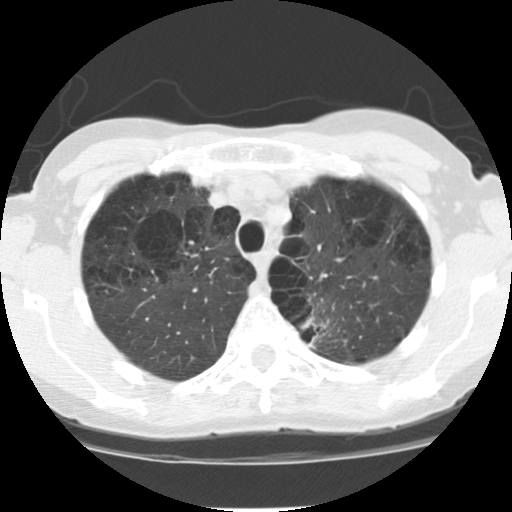
Low-dose screening chest CT, one axial slice. Position 92 of 116 along the scan axis. Reconstruction kernel STANDARD. Lung window (W 1500 / L -600 HU). 2.5 mm slice thickness. 512 × 512 image matrix, field of view 300 × 300 mm.
Outlined on this slice (manually delineated by an expert):
- lesion 1 (tumor, upper lobe of left lung): bounding box (x1, y1, x2, y2) in pixels: (301, 316, 329, 349)